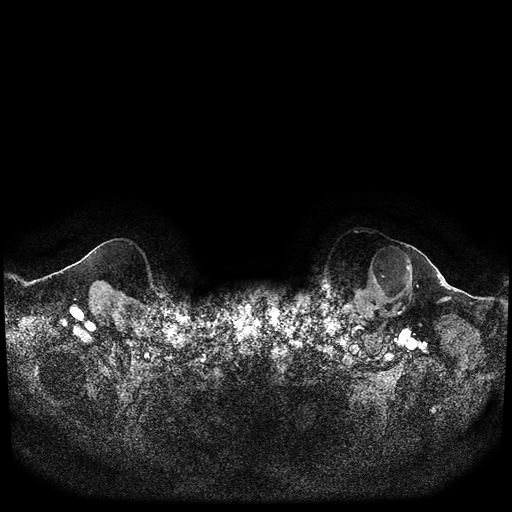
Breast MRI (dynamic contrast-enhanced, multi-phase), one axial slice. Slice 103 of 116 in the series (ordered by position). Dynamic contrast-enhanced series, time point 2 of 5 at this slice position (early post-contrast). 1.5 T. TE 2.6 ms, TR 5.3 ms. 512 × 512 image matrix, field of view 350 × 350 mm. Patient: female, 64 years.
Structures marked on this image (semi-automatic segmentation, software-assisted and operator-edited):
- breast lesion (labelled 'tumour' in the annotation; benign lesions carry a separate 'benign' label): box from (x=366, y=245) to (x=413, y=297) px